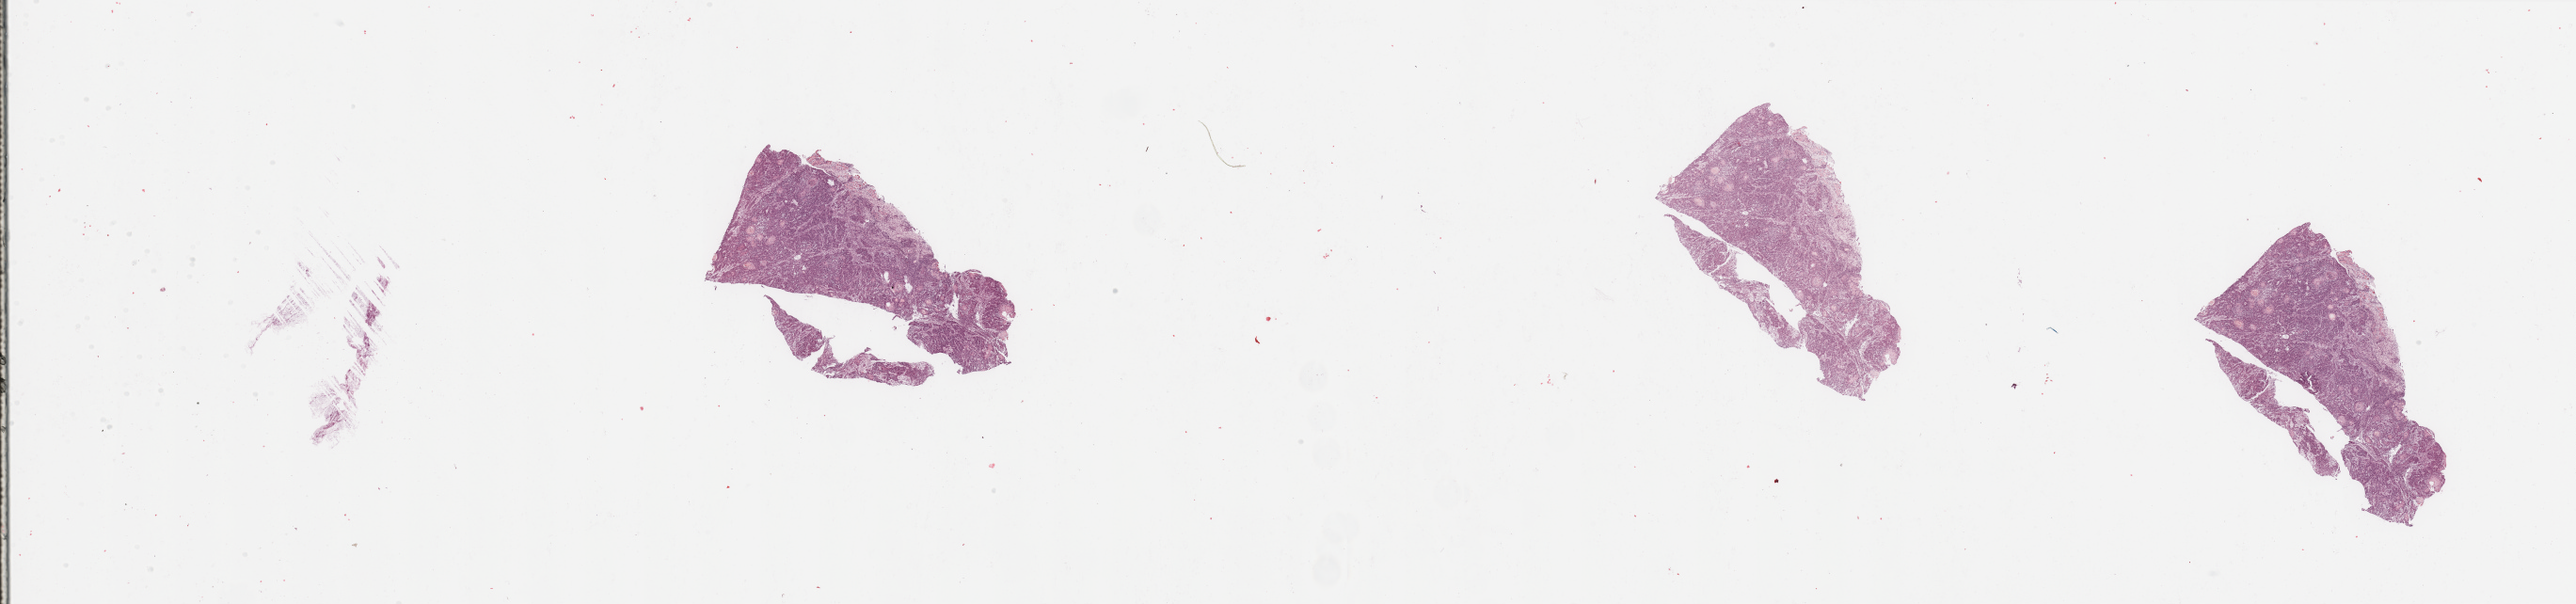
H&E whole-slide image — low-resolution overview of the scanned area, about 43.3 x 10.2 mm (from a 20x scan), tumour tissue sample, sampled site: floor of mouth. Male, 65 y/o. Histologic grade: G2 (moderately differentiated). Slide review estimates, as recorded: tumour nuclei 85%, necrosis 2%.
• AJCC pathologic stage: II
• primary tumour site (as recorded): oral cavity
• histologic diagnosis: Squamous cell carcinoma, NOS (floor of mouth, NOS)